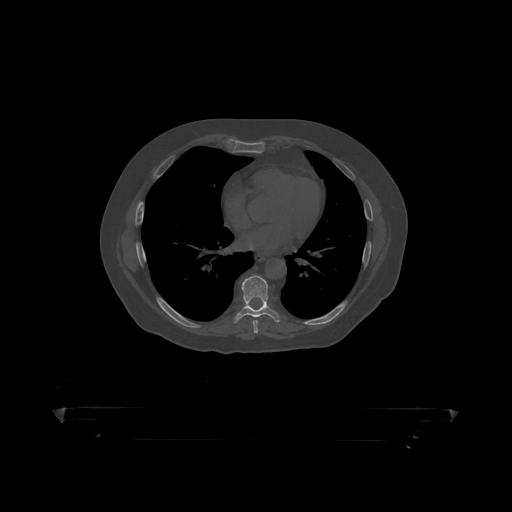
CT including the spine, one axial slice. Position 260 of 390 along the scan axis. Reconstruction kernel STANDARD. 120 kVp. Bone window (W 1800 / L 400 HU). 512 × 512 image matrix. Male patient, age 60 years. Case-level facts recorded for this patient, not image findings: primary cancer: prostate.
Structures marked on this image (semi-automatically segmented with operator editing):
- T8 vertebra: bounding box (x1, y1, x2, y2) in pixels: (236, 275, 278, 318)